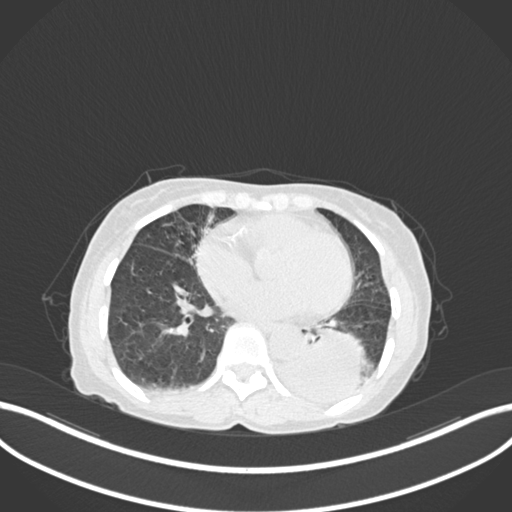
Chest CT, one axial slice; position 48 of 233 along the scan axis; reconstruction kernel B30f; lung window (W 1500 / L -600 HU); 1 mm slice thickness; 512 × 512 image matrix, field of view 400 × 400 mm. Patient: female, 78 years. From the clinical record (not read from this slice): clinical TNM (as recorded): T3 N0 M1.
Structures marked on this image (rectangle marked by the reading radiologist):
- lung tumour (recorded histology: squamous cell carcinoma): bounding box (x1, y1, x2, y2) in pixels: (276, 322, 373, 403)